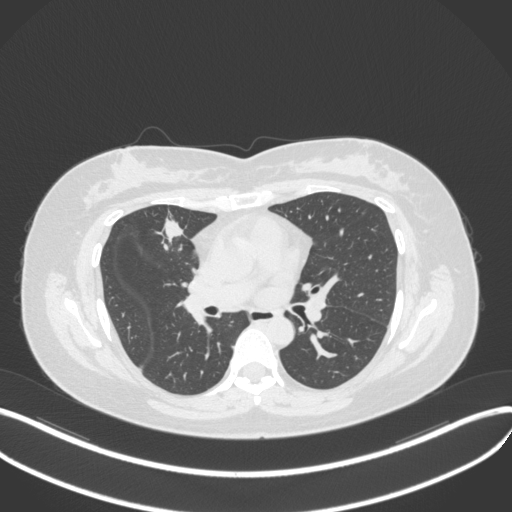
Chest CT, one axial slice. Position 172 of 272 along the scan axis. Reconstruction kernel B31f. 120 kVp. Lung window (W 1500 / L -600 HU). 1 mm slice thickness. 512 × 512 image matrix, field of view 400 × 400 mm. Female patient, age 42 years. From the clinical record (not read from this slice): clinical TNM (as recorded): T1b N0 M0.
Structures marked on this image (rectangle marked by the reading radiologist):
- lung tumour (recorded histology: adenocarcinoma): bounding box <155,214,189,250> (left, top, right, bottom; pixels)